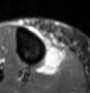
MRI of an extremity soft-tissue mass, one axial slice; STIR; MR volume resampled by the dataset authors to the PET/CT grid (not the native acquisition matrix); 3.27 mm slice thickness; 90 × 93 image matrix, field of view 88 × 91 mm. Female patient. Case-level facts recorded for this patient, not image findings: histological type: undifferentiated – high grade; grade: high; site of the primary tumour: right thigh.
Outlined on this slice (expert contour drawn on MRI and transferred to this co-registered scan by the dataset authors):
- gross tumour volume (mass): bounding box <37,42,66,75> (left, top, right, bottom; pixels)